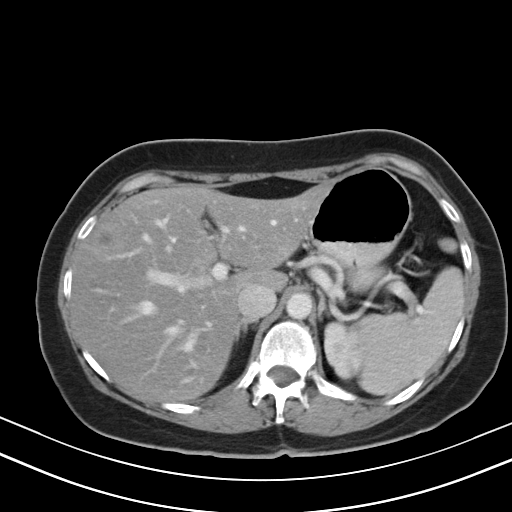
Contrast-enhanced abdominal CT, one axial slice. Position 32 of 47 along the scan axis. 130 kVp. Soft-tissue window (W 400 / L 40 HU). 5 mm slice thickness. 512 × 512 image matrix. Female patient. Case-level facts recorded for this patient, not image findings: diagnosis: colorectal cancer liver metastases, imaged before liver resection; multiple liver metastases: no.
Structures marked on this image (manually delineated by an expert):
- hepatic veins: bounding box [x1, y1, x2, y2] px = [126, 219, 275, 359]
- liver: [74, 189, 324, 400]
- planned liver remnant (the part of the liver to remain after resection): [74, 189, 324, 400]
- portal vein (with intrahepatic branches): [111, 227, 230, 350]
- liver metastasis: [97, 231, 113, 247]